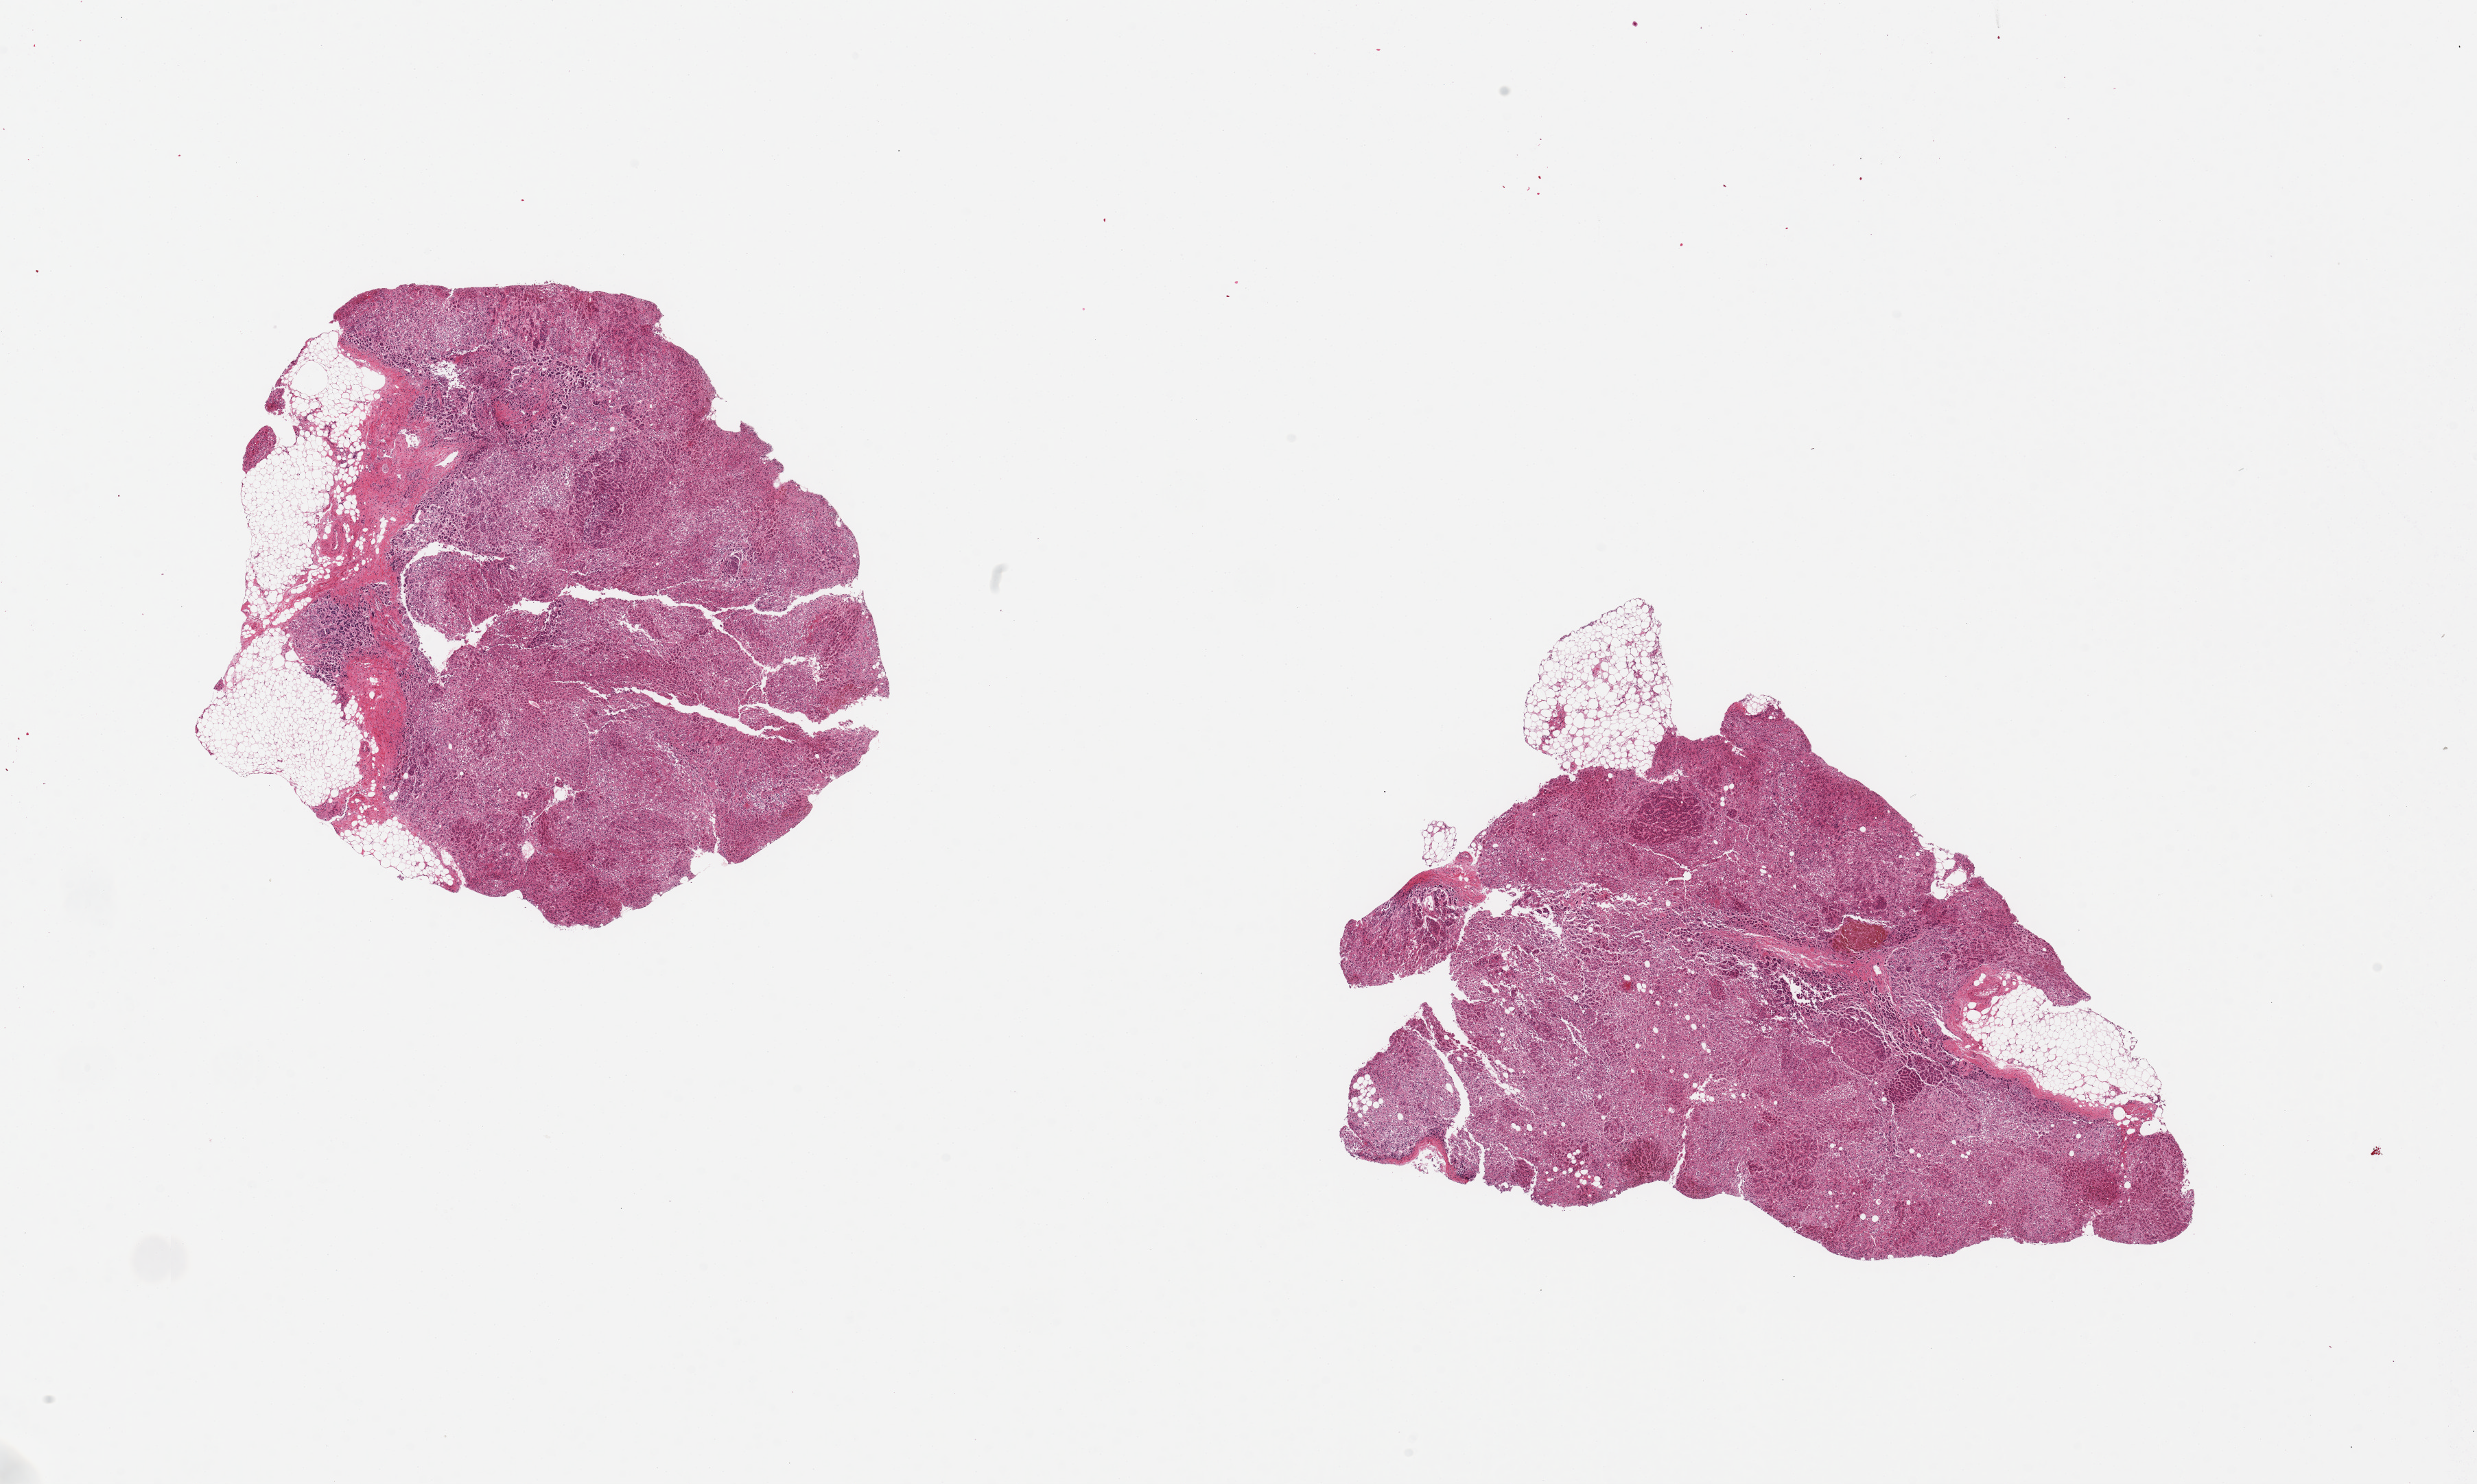
H&E whole-slide image — a low-resolution overview of the entire scanned area, about 28.5 x 17.1 mm. PAXgene-fixed, paraffin-embedded tissue. Target tissue: adrenal gland. Tissue donor sample.
Review note (as recorded): 2 pieces, 6.6x6.5 & 7x8mm; ~10% adipose.